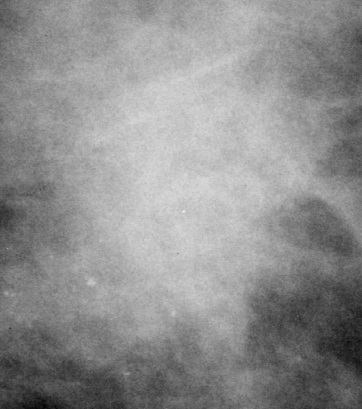
Cropped region of a digitized screen-film mammogram centred on a radiologist-marked abnormality, left breast, MLO view.
Mass, shape irregular / architectural distortion, margins obscured / spiculated; BI-RADS assessment category 4; subtlety rating 4 on a 1 (subtle) to 5 (obvious) scale; pathology (as recorded): malignant.